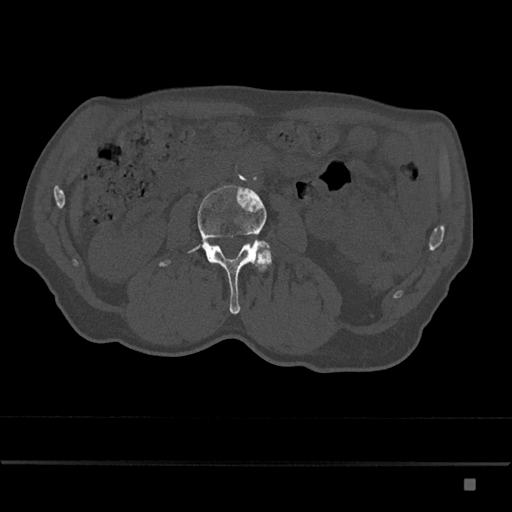
CT including the spine, one axial slice; slice 402 of 797 in the series (ordered by position); reconstruction kernel Br40s/3; 120 kVp; bone window (W 1800 / L 400 HU); 0.5 mm slice thickness; 512 × 512 image matrix. Patient: male, 72 years. From the clinical record (not read from this slice): primary cancer: prostate.
Outlined on this slice (semi-automatic segmentation, software-assisted and operator-edited):
- L3 vertebra: bounding box (x1, y1, x2, y2) in pixels: (159, 185, 270, 314)
- L4 vertebra: (256, 248, 272, 271)